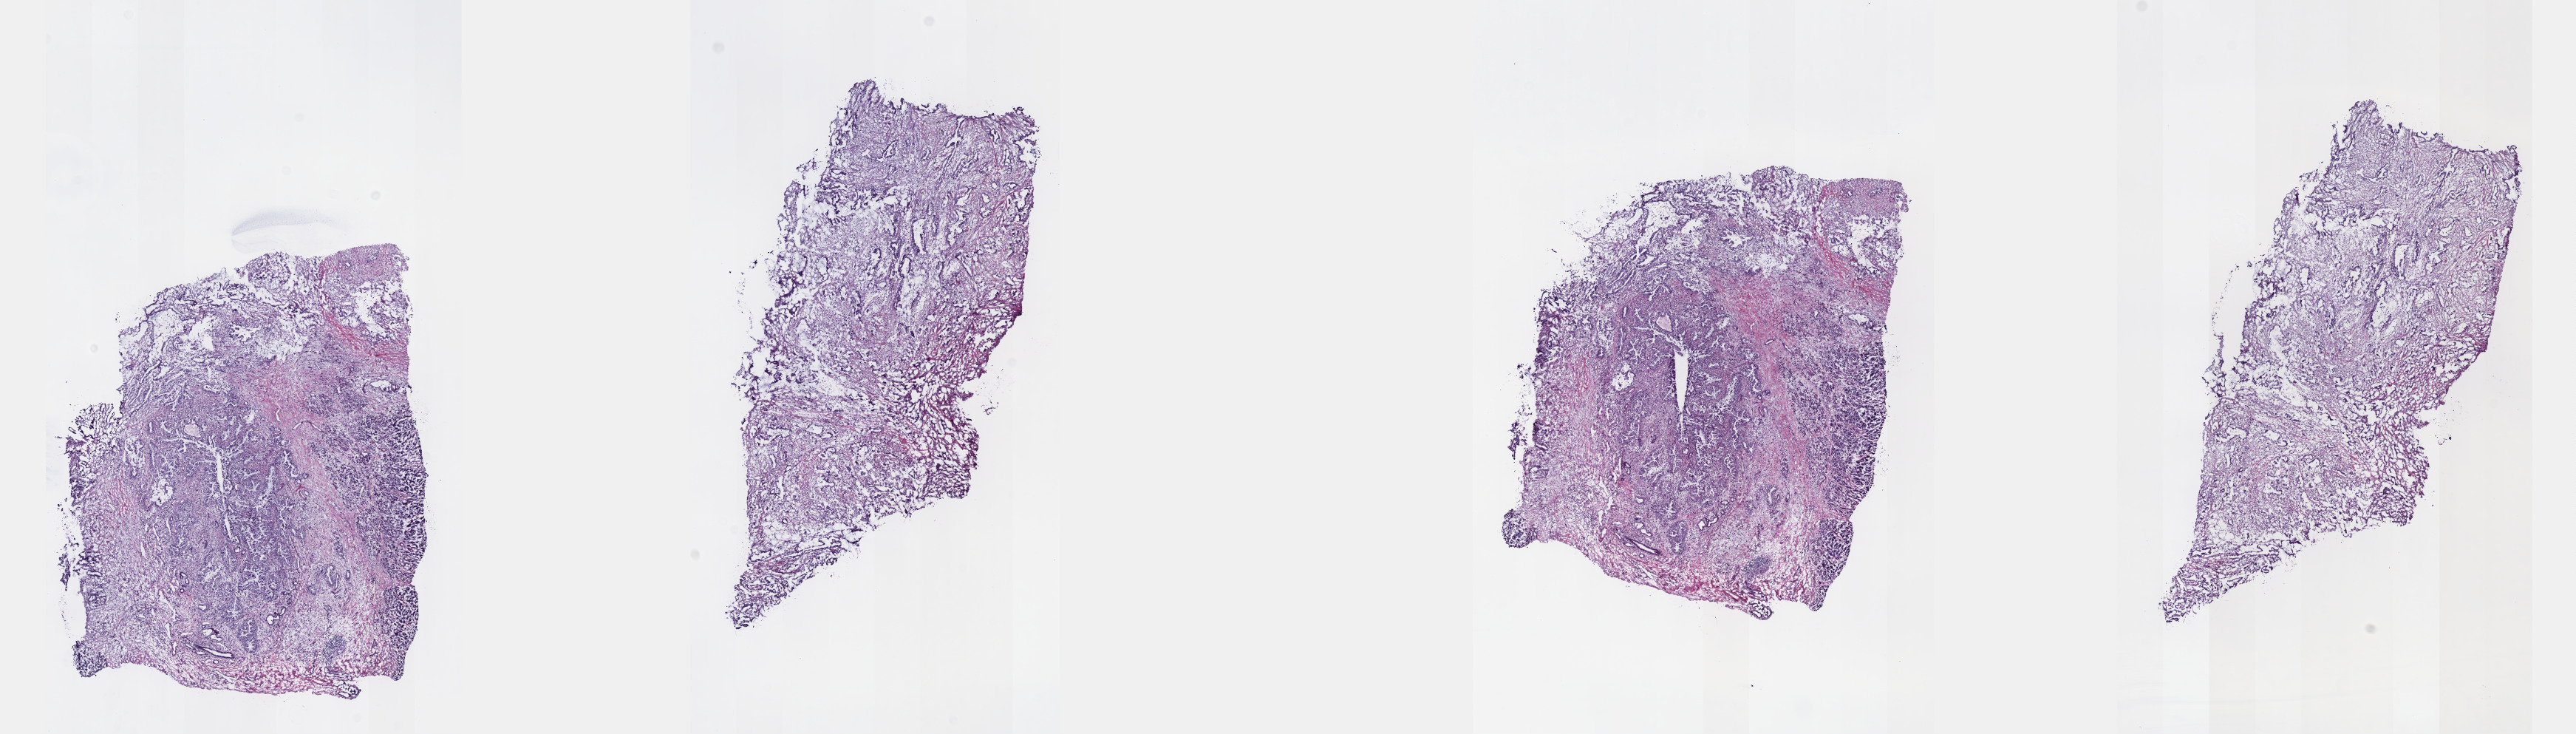
Hematoxylin and eosin (H&E) stained whole-slide image — low-resolution overview of the scanned area, about 28.2 x 8.0 mm (from a 40x scan). Frozen section. Sample: primary tumour, pancreas. Patient: female, age at initial diagnosis 61 years. Histologic grade: G2 (moderately differentiated). Slide review estimates, as recorded: tumour cells 80%, tumour nuclei 80%, normal cells 0%, stromal cells 20%, necrosis 0%. Inflammatory infiltration, as recorded: lymphocyte infiltration 40%, monocyte infiltration 20%, neutrophil infiltration 20%.
AJCC pathologic stage: IIB. Diagnosis: Infiltrating duct carcinoma, NOS.